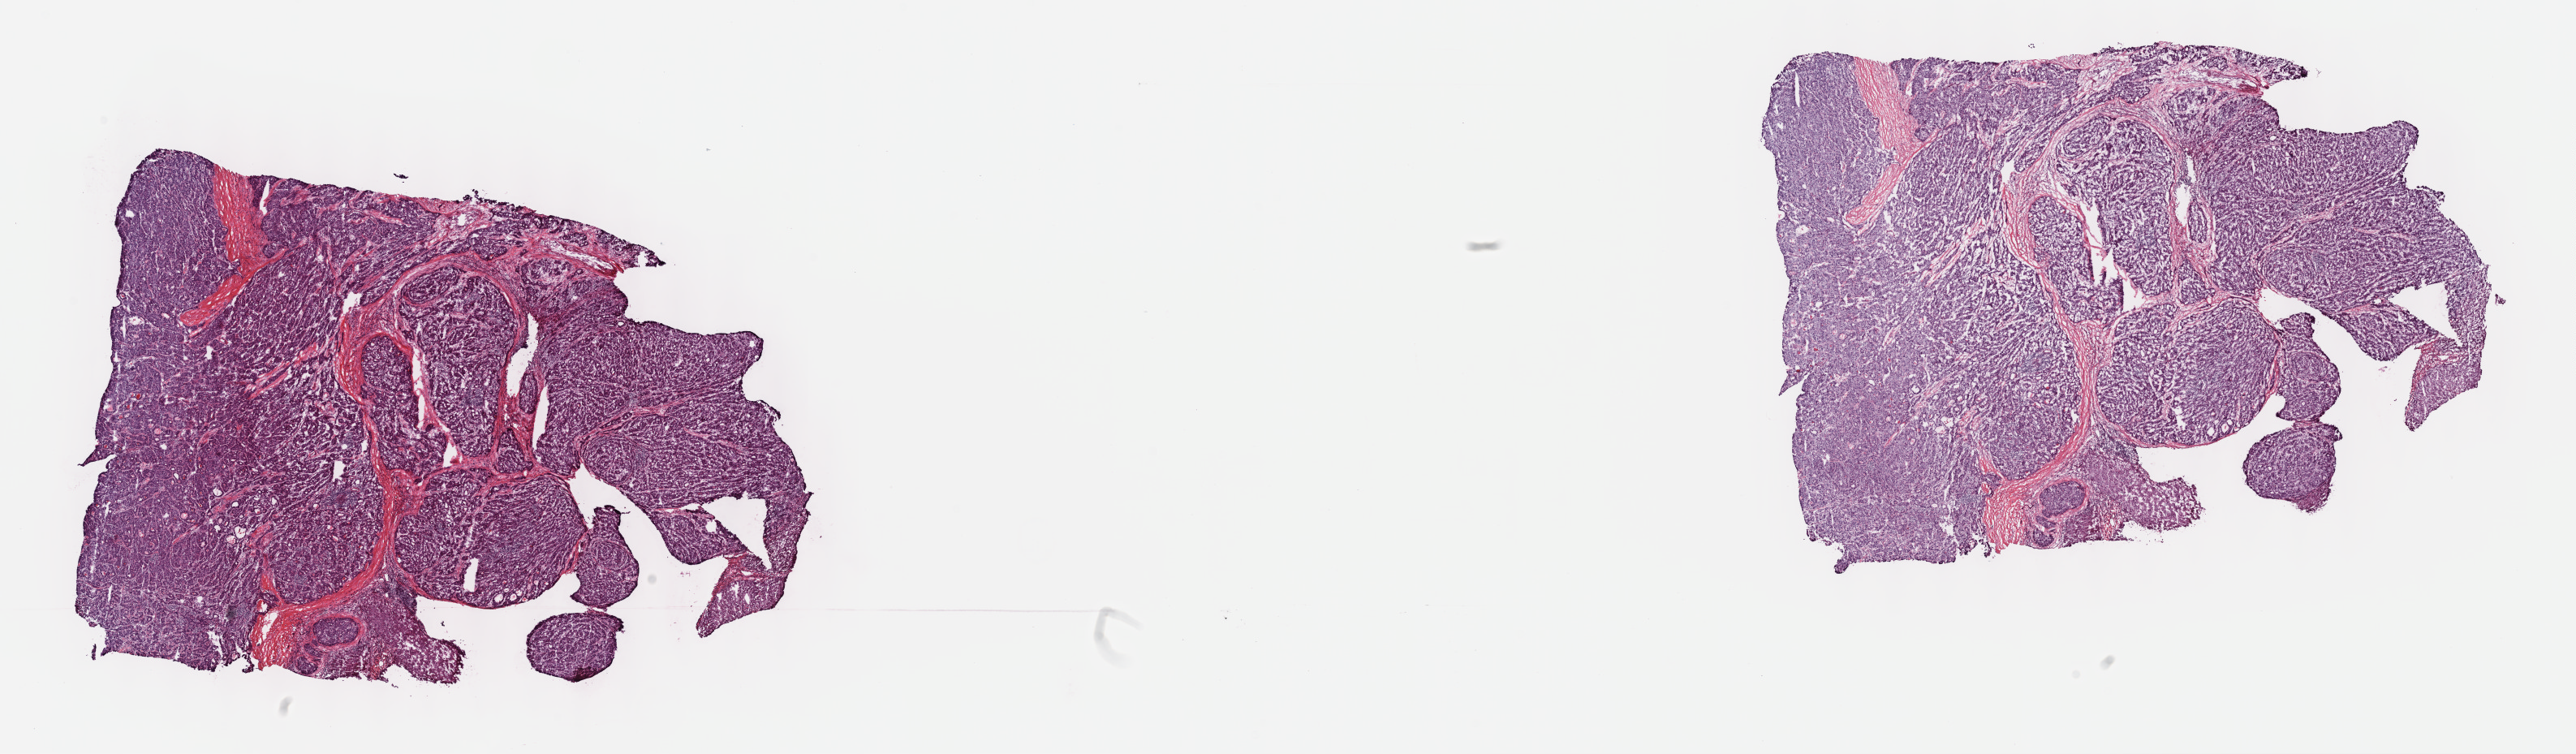
Hematoxylin and eosin (H&E) stained whole-slide image — a low-resolution overview of the entire scanned area, about 25.7 x 7.5 mm (slide scanned at 40x). Frozen section. Primary tumour sample from the liver. Male patient; age at initial diagnosis 51 years. Histologic grade: G2 (moderately differentiated). Slide review estimates, as recorded: tumour cells 85%, tumour nuclei 90%, normal cells 0%, stromal cells 15%, necrosis 0%. Infiltration values recorded for this section: lymphocyte infiltration 0%, monocyte infiltration 0%, neutrophil infiltration 0%.
- histologic diagnosis: Hepatocellular carcinoma, NOS
- AJCC pathologic stage: I